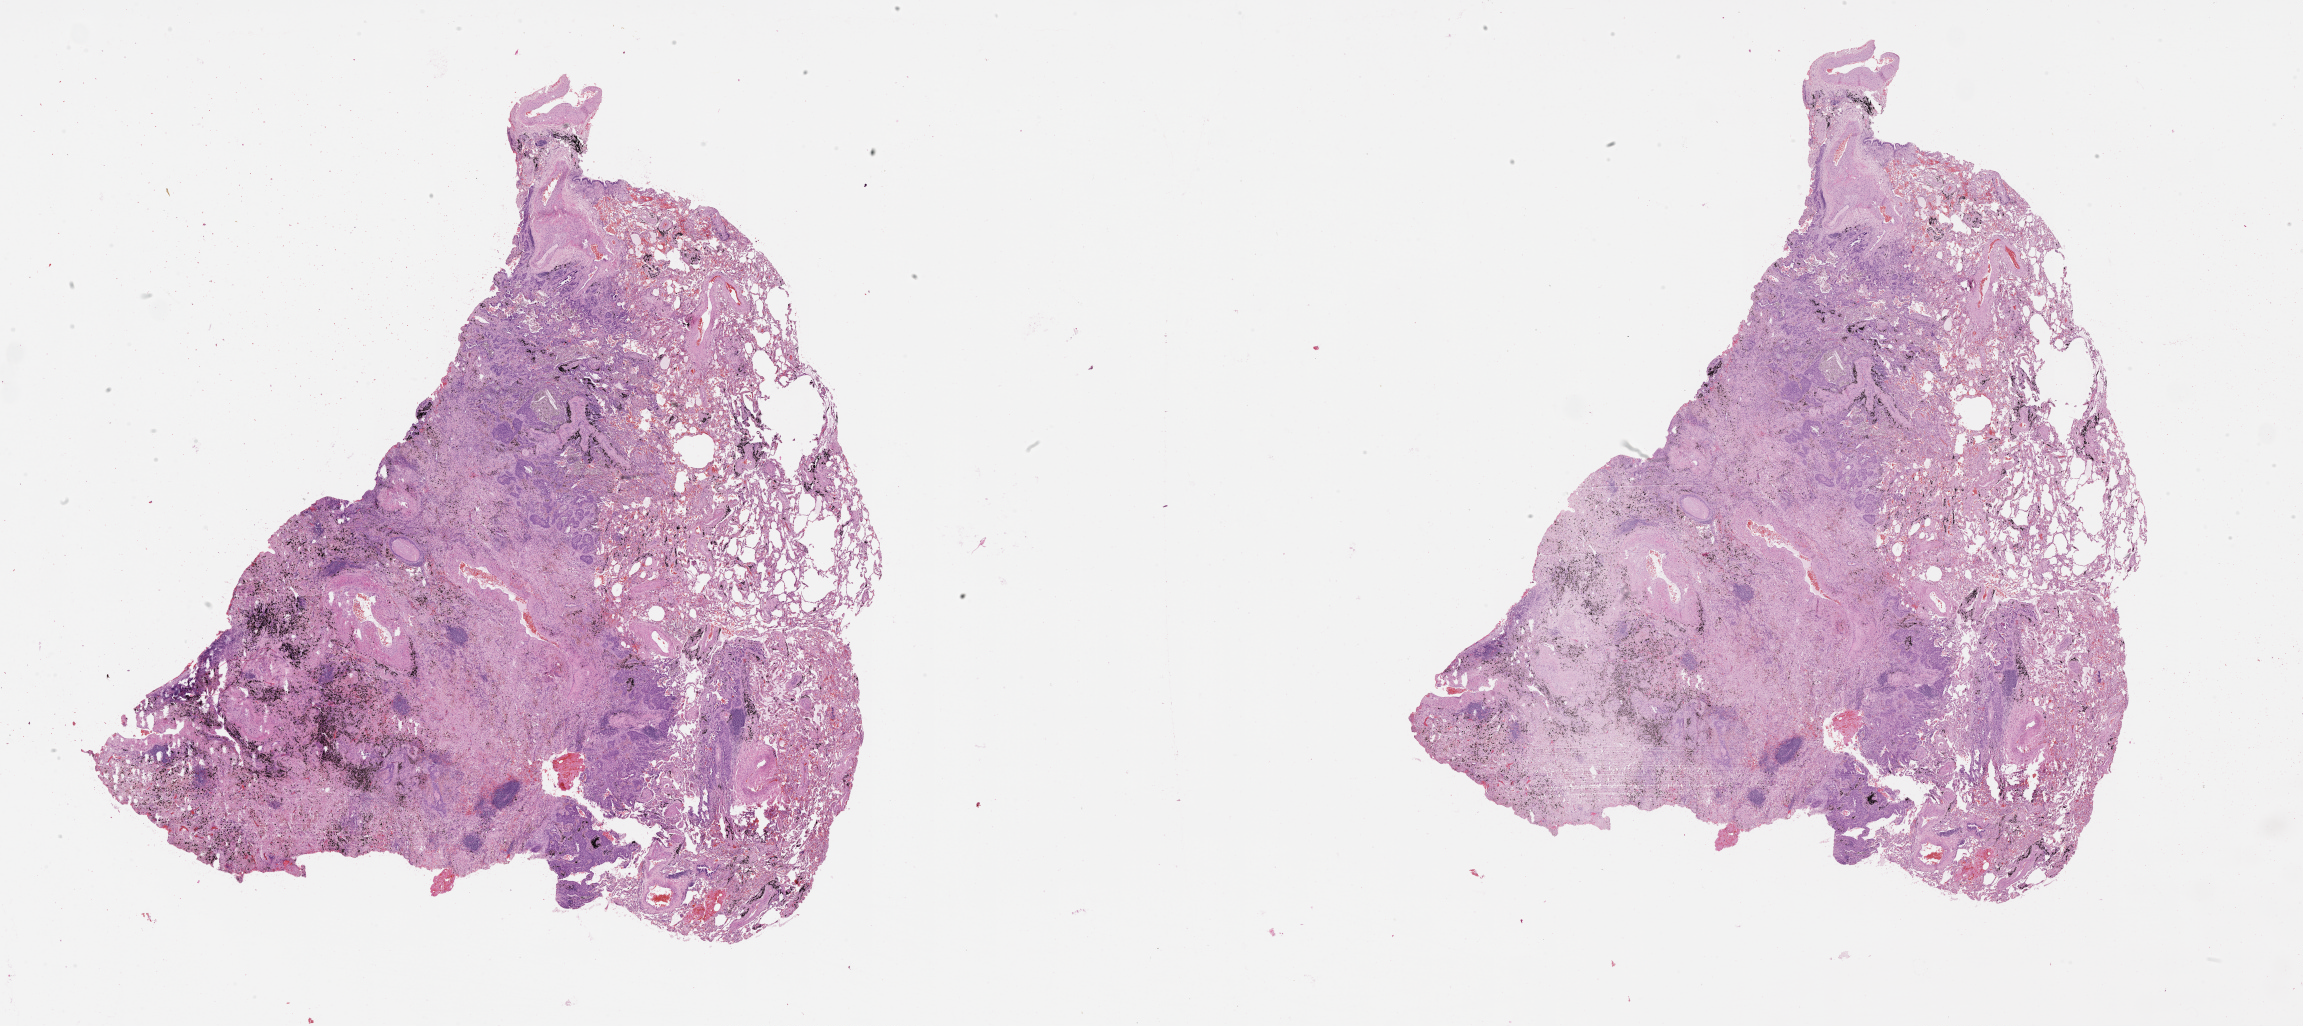
H&E-stained whole-slide image — shown as a low-resolution overview of the whole scanned area (about 37.1 x 16.5 mm, acquisition: 20x scan); lung, tissue type not recorded.
Patient diagnosis (cohort enrolment): squamous cell carcinoma (lung).